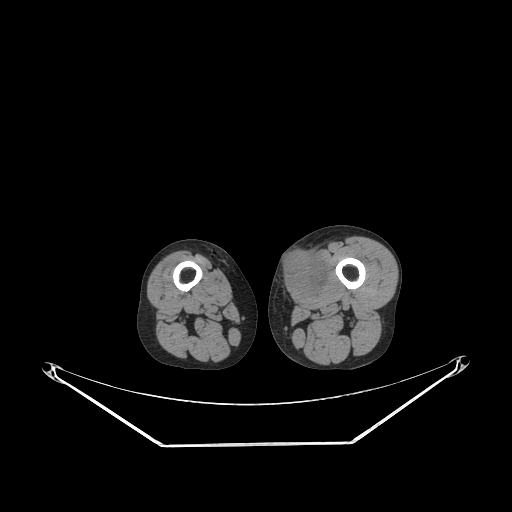
CT of an extremity soft-tissue mass (from a PET/CT study), one axial slice. Slice 213 of 267 in the series (ordered by position). 140 kVp. Soft-tissue window (W 400 / L 40 HU). 3.75 mm slice thickness. 512 × 512 image matrix, field of view 500 × 500 mm. Male patient. Case-level facts recorded for this patient, not image findings: histological type: pleiomorphic leiomyosarcoma; grade: high; site of the primary tumour: left thigh.
Outlined on this slice (expert contour drawn on MRI and transferred to this co-registered scan by the dataset authors):
- gross tumour volume including surrounding oedema: bounding box [x1, y1, x2, y2] px = [281, 251, 328, 298]
- gross tumour volume (mass): [281, 253, 325, 298]